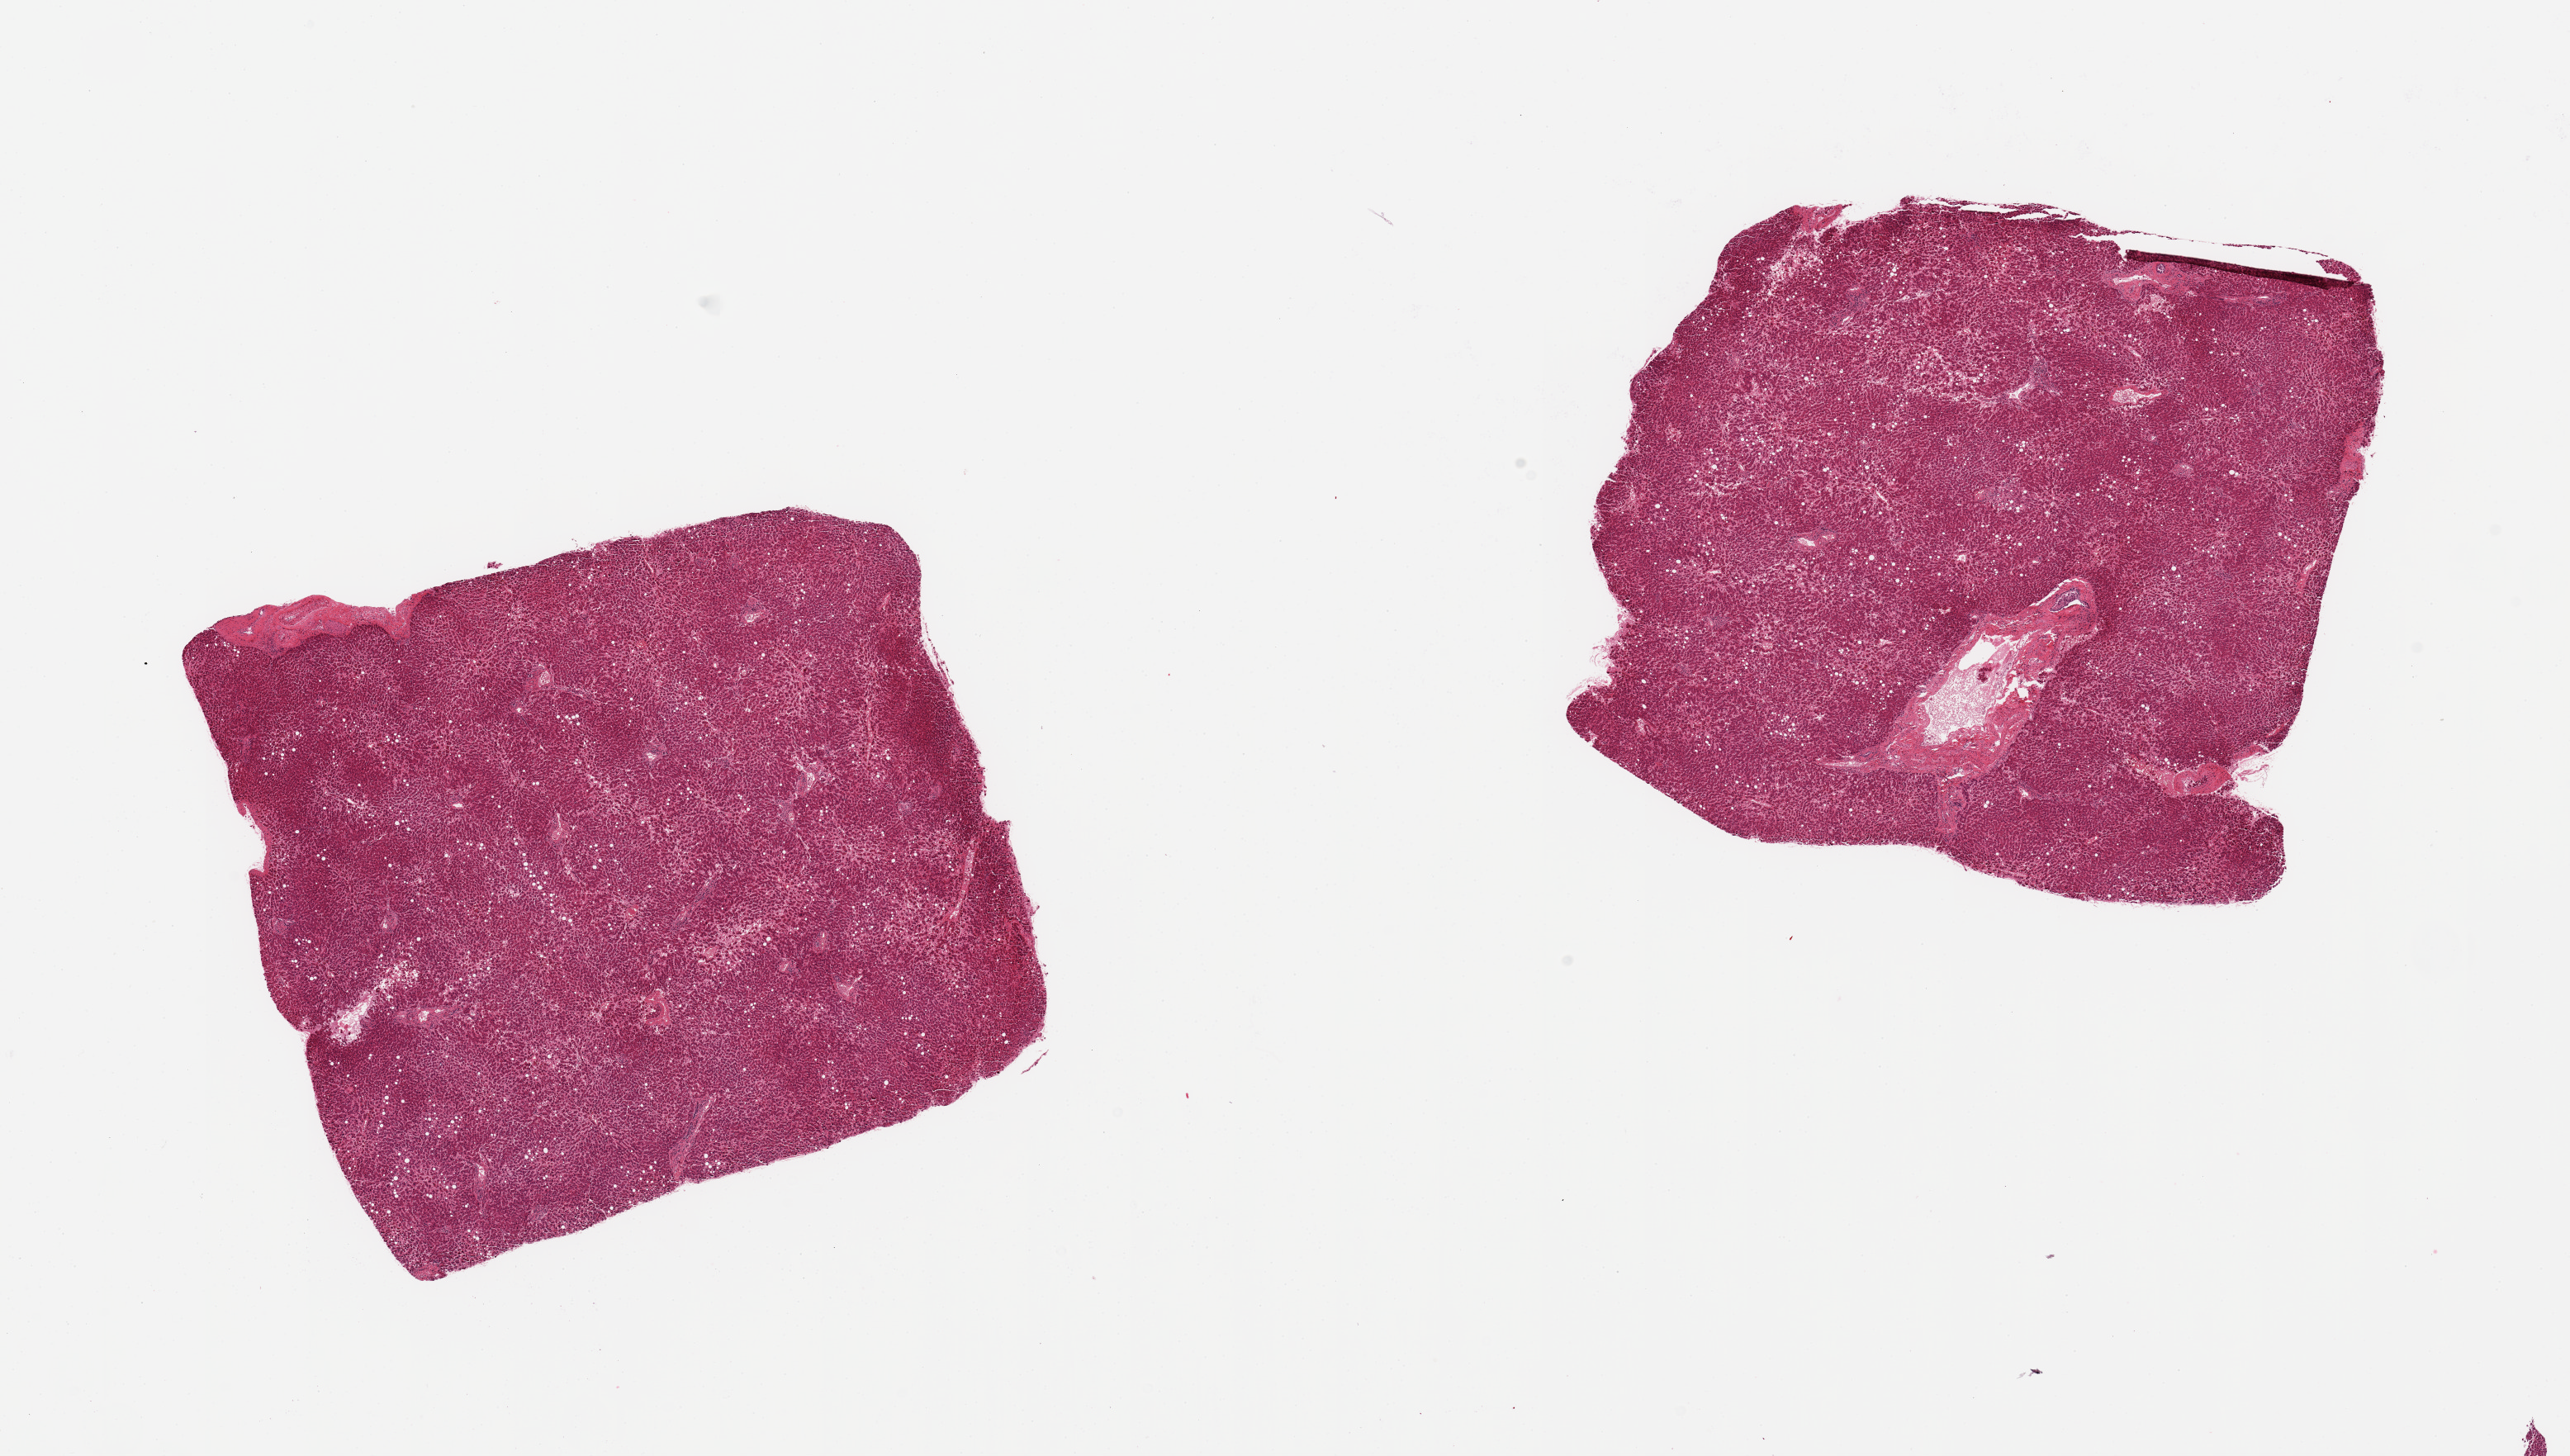
Digitized H&E-stained section, brightfield, low-resolution overview of the scanned area, about 24.6 x 13.9 mm, PAXgene-fixed, paraffin-embedded tissue, sampled site (target tissue): liver, tissue donor sample. Donor: male.
* review note (as recorded): 2 pieces; mild steatosis